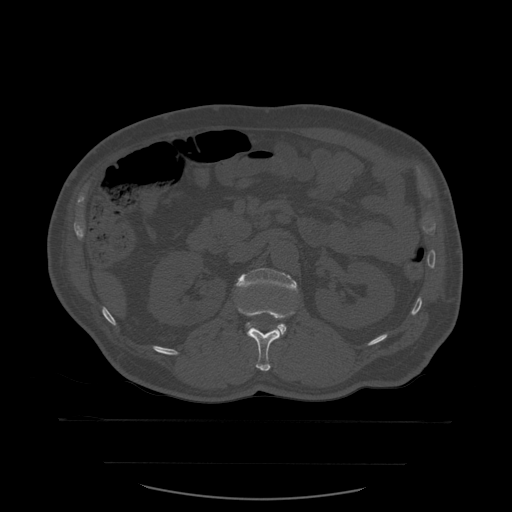
CT including the spine, one axial slice; slice 236 of 590 in the series (ordered by position); bone window (W 1800 / L 400 HU); 1.25 mm slice thickness; 512 × 512 image matrix. Patient age 71 years. From the clinical record (not read from this slice): primary cancer: lung.
Outlined on this slice (semi-automatic segmentation, software-assisted and operator-edited):
- L1 vertebra: bounding box <238,307,295,371> (left, top, right, bottom; pixels)
- L2 vertebra: <236,268,298,336>